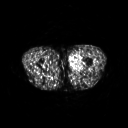
FDG PET of an extremity soft-tissue mass (from a PET/CT study), one axial slice; position 242 of 311 along the scan axis; 3.27 mm slice thickness; 128 × 128 image matrix, field of view 500 × 500 mm. Male patient, age 29 years. From the clinical record (not read from this slice): histological type: mixoid liposarcoma; grade: low; site of the primary tumour: left thigh.
Annotated regions visible in this slice (expert contour drawn on MRI and transferred to this co-registered scan by the dataset authors):
- gross tumour volume (mass): bounding box [x1, y1, x2, y2] px = [69, 54, 82, 69]